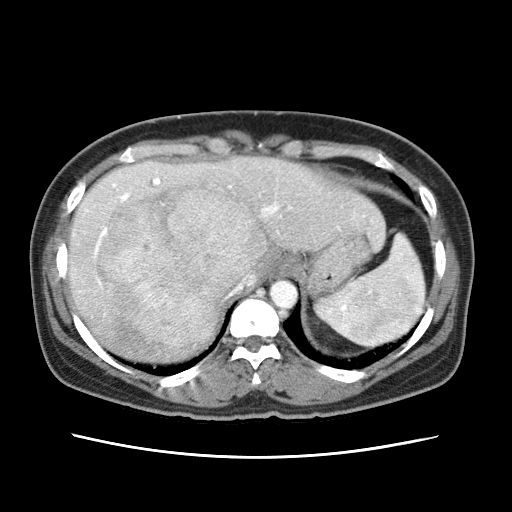
Contrast-enhanced abdominal CT (liver protocol), one axial slice. Slice 52 of 79 in the series (ordered by position). Reconstruction kernel STANDARD. 120 kVp. Soft-tissue window (W 400 / L 40 HU). 2.5 mm slice thickness. 512 × 512 image matrix, field of view 340 × 340 mm. From the clinical record (not read from this slice): diagnosis: hepatocellular carcinoma (patient treated with transarterial chemoembolisation; whether this scan precedes or follows treatment is not stated here); TNM stage (as recorded): Stage-I; Child-Pugh class: A; tumour differentiation: moderately differentiated; tumour nodularity: uninodular.
Structures marked on this image (semi-automatic segmentation, software-assisted and operator-edited):
- abdominal aorta: bounding box (x1, y1, x2, y2) in pixels: (271, 280, 298, 309)
- liver parenchyma outside the tumour (the mass and vessels are separate outlines, so this box may not span the whole liver): (68, 158, 383, 360)
- mass: (98, 179, 267, 345)
- liver vessels: (85, 178, 279, 285)